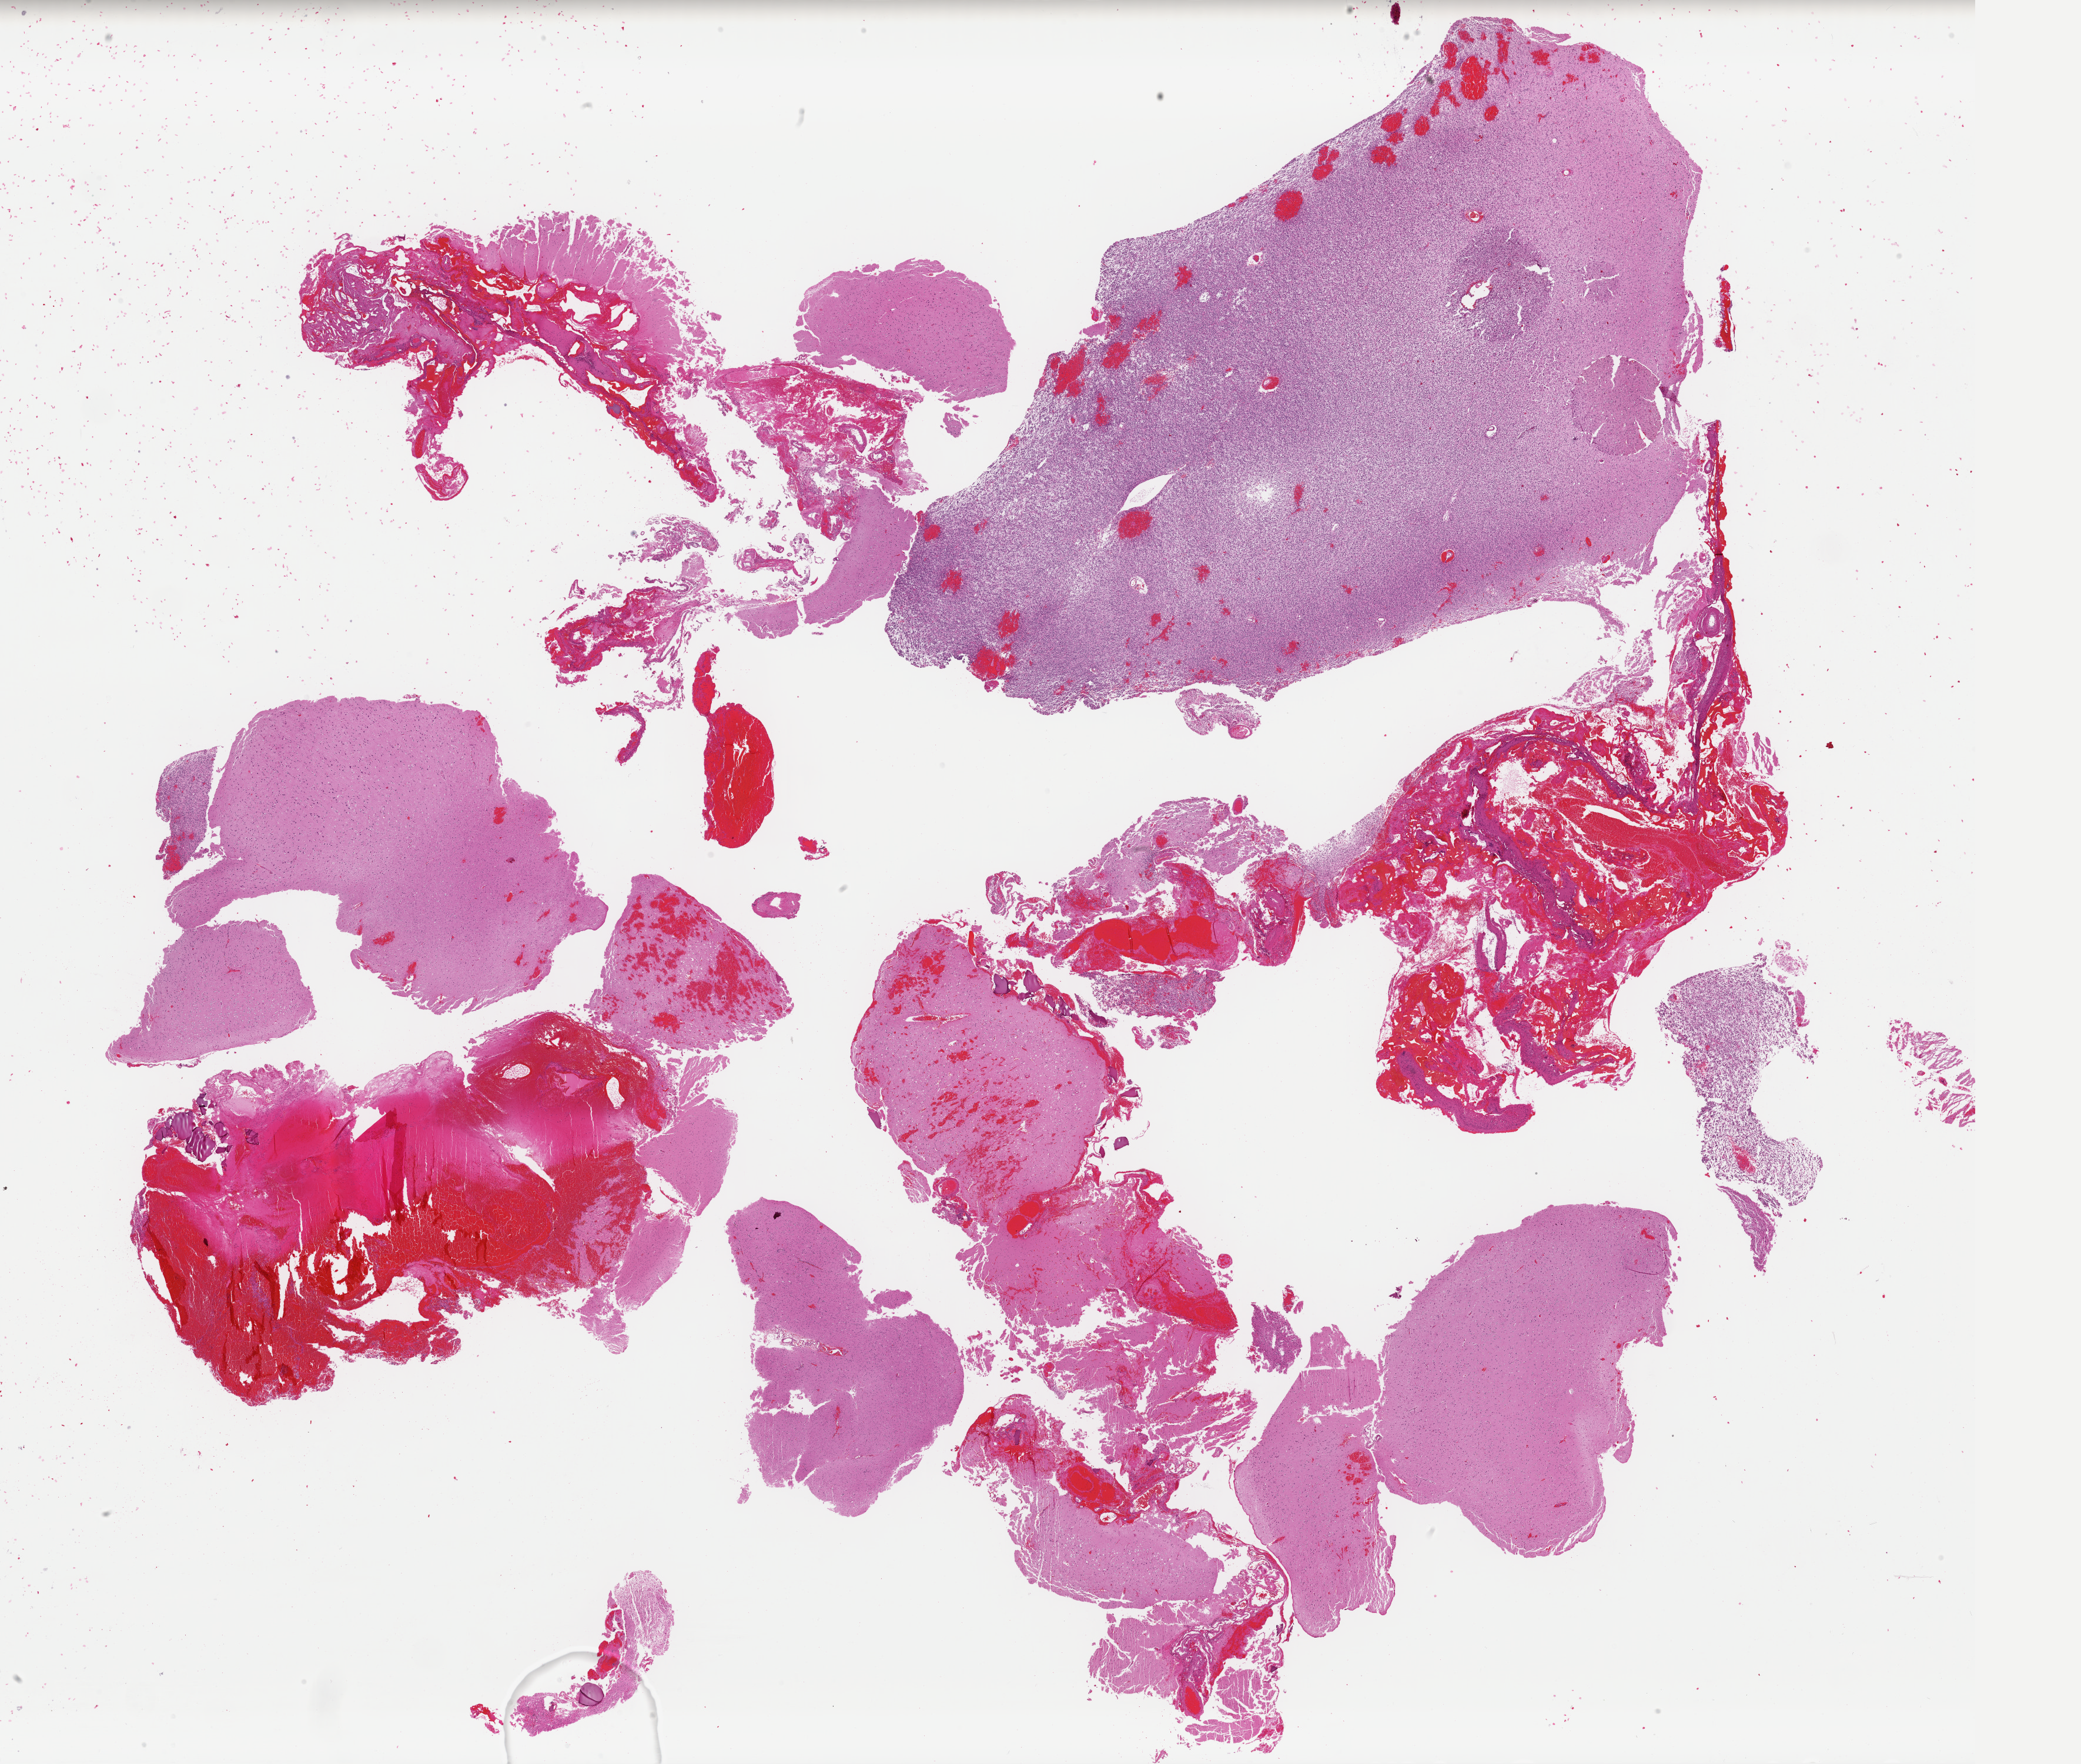
Digitized H&E-stained tissue section (whole slide), shown as a low-resolution overview of the whole scanned area (about 28.0 x 23.7 mm, from a 40x scan). Formalin-fixed paraffin-embedded (FFPE) diagnostic section. Brain, recurrent tumour sample. Female, age 27 years at initial diagnosis.
This section: recurrent tumour. Patient diagnosis: Oligodendroglioma, NOS (temporal lobe).